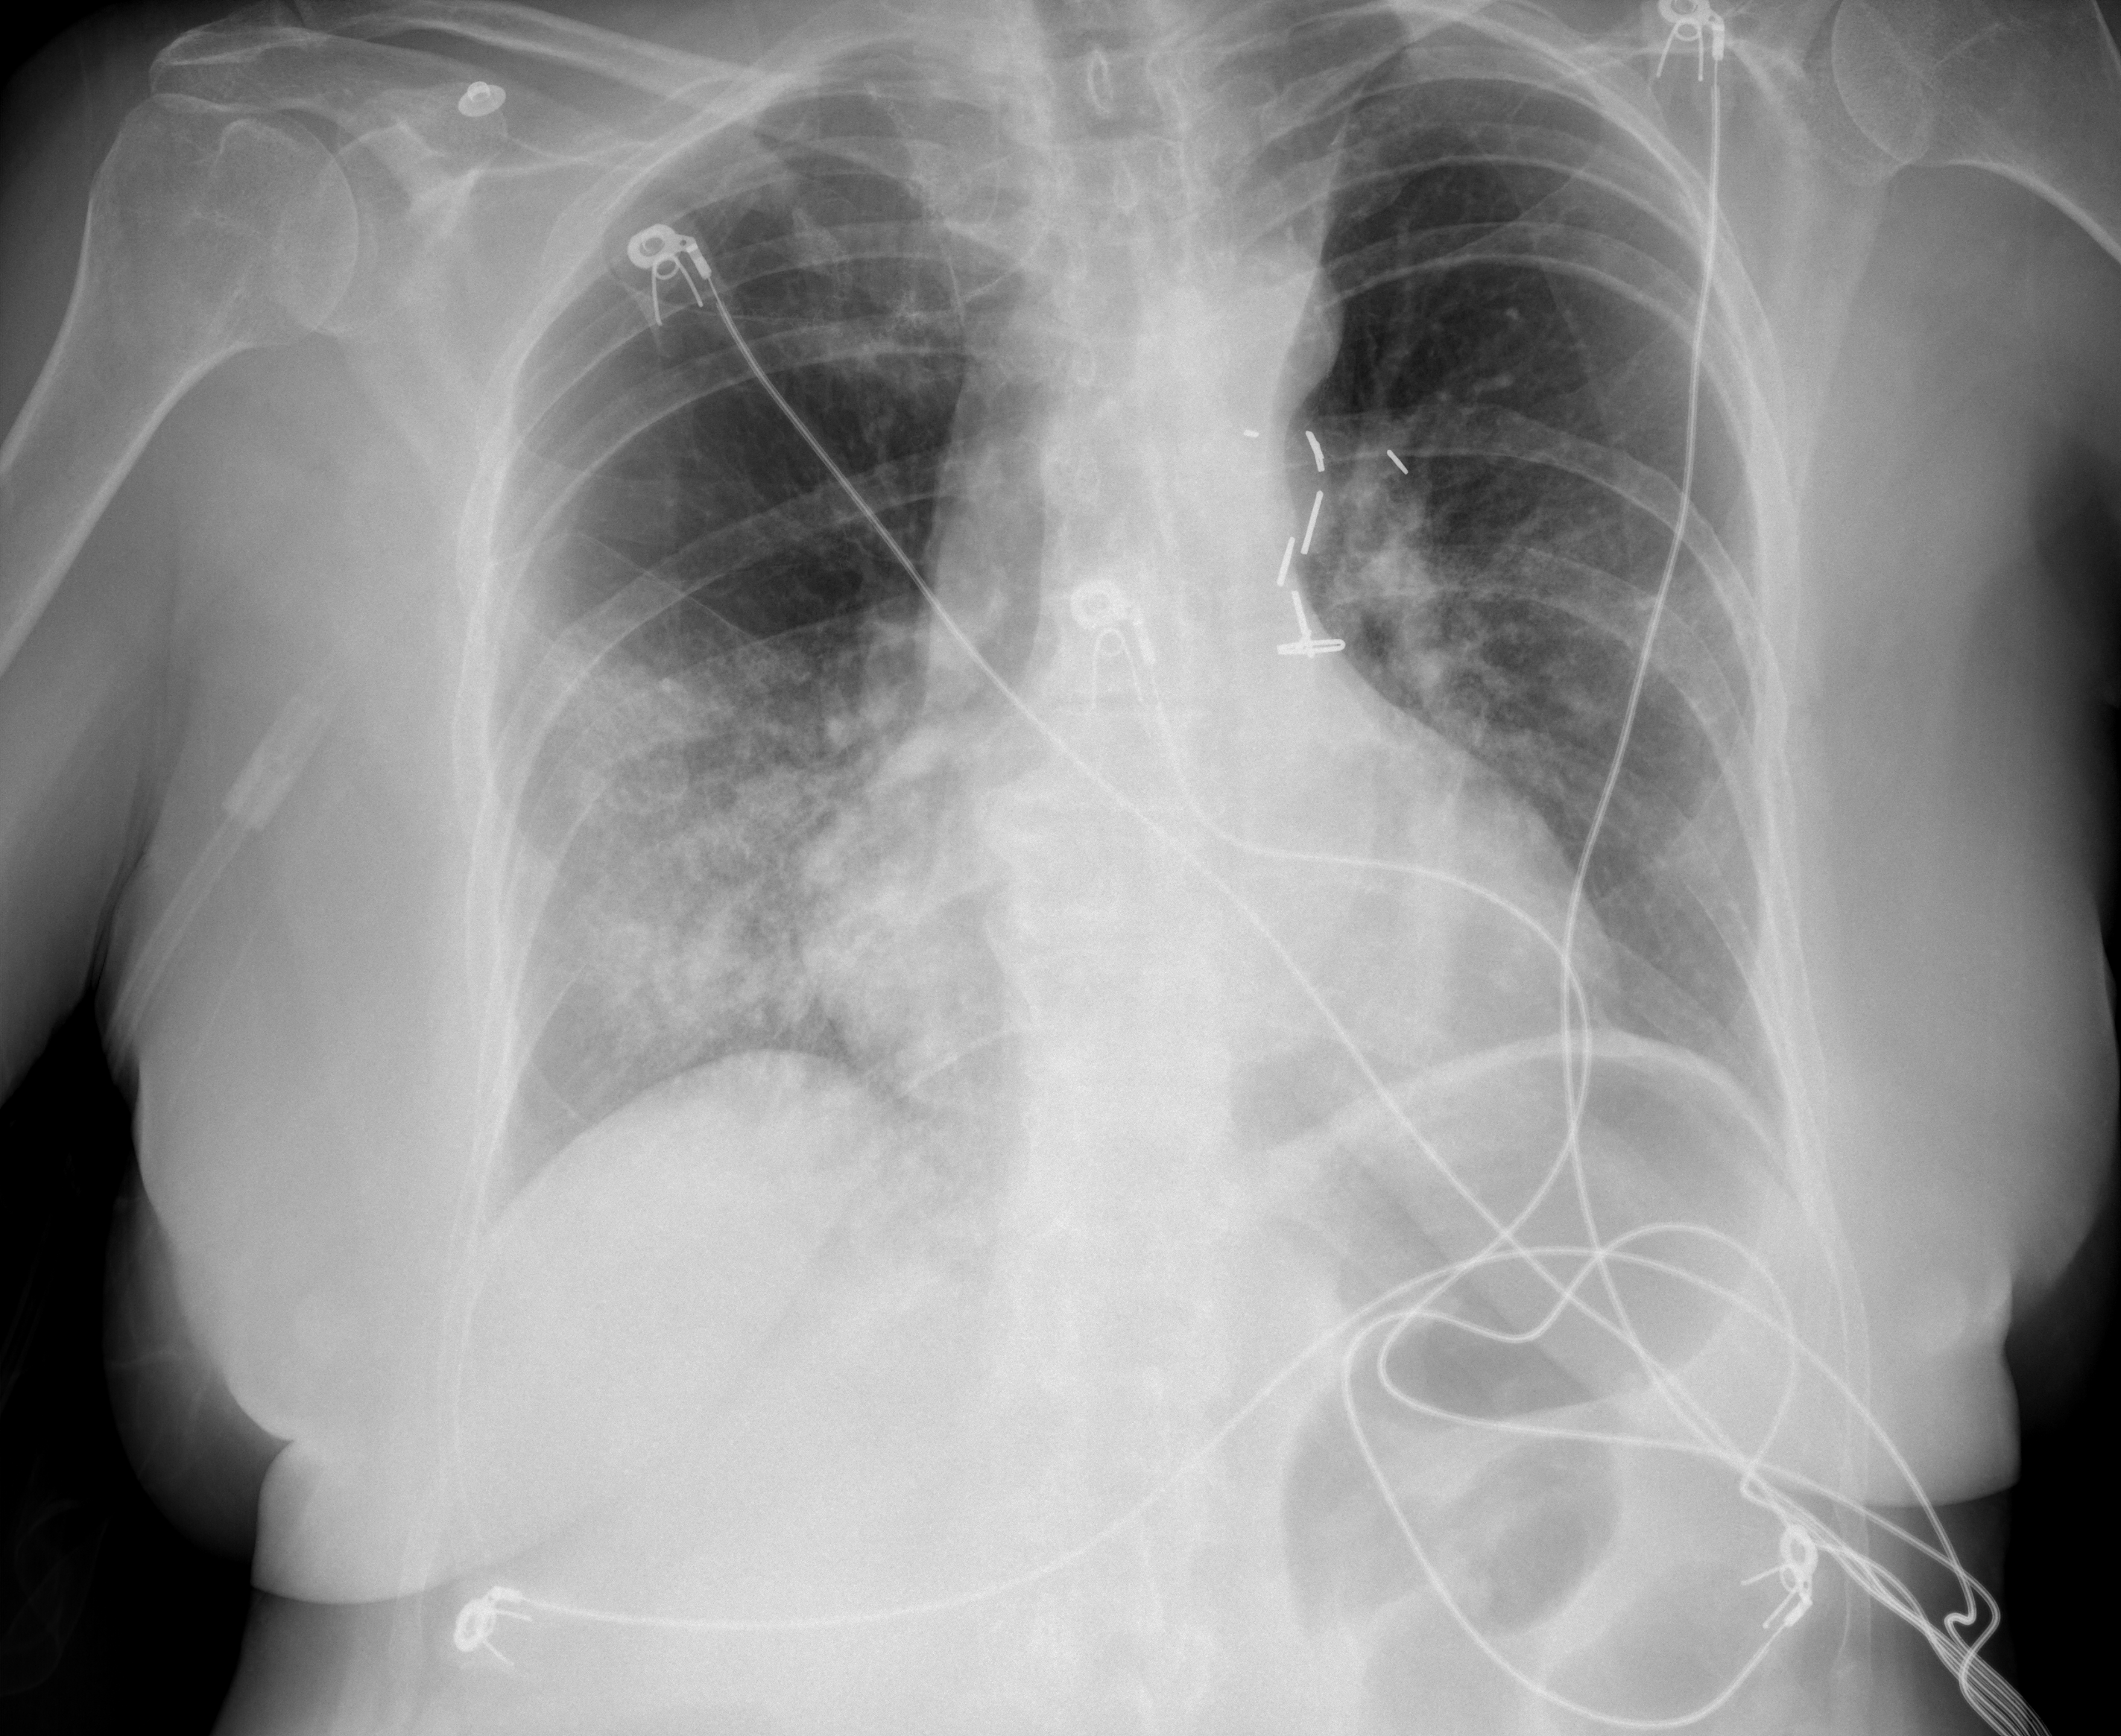
Chest X-ray (portable), AP projection. Female patient, age 72 years; imaged 1 day after the COVID-19 diagnosis.
Radiologist key findings (as recorded): Hazy airspace opacities are seen throughout the bilateral lower lungs, right greater than left.